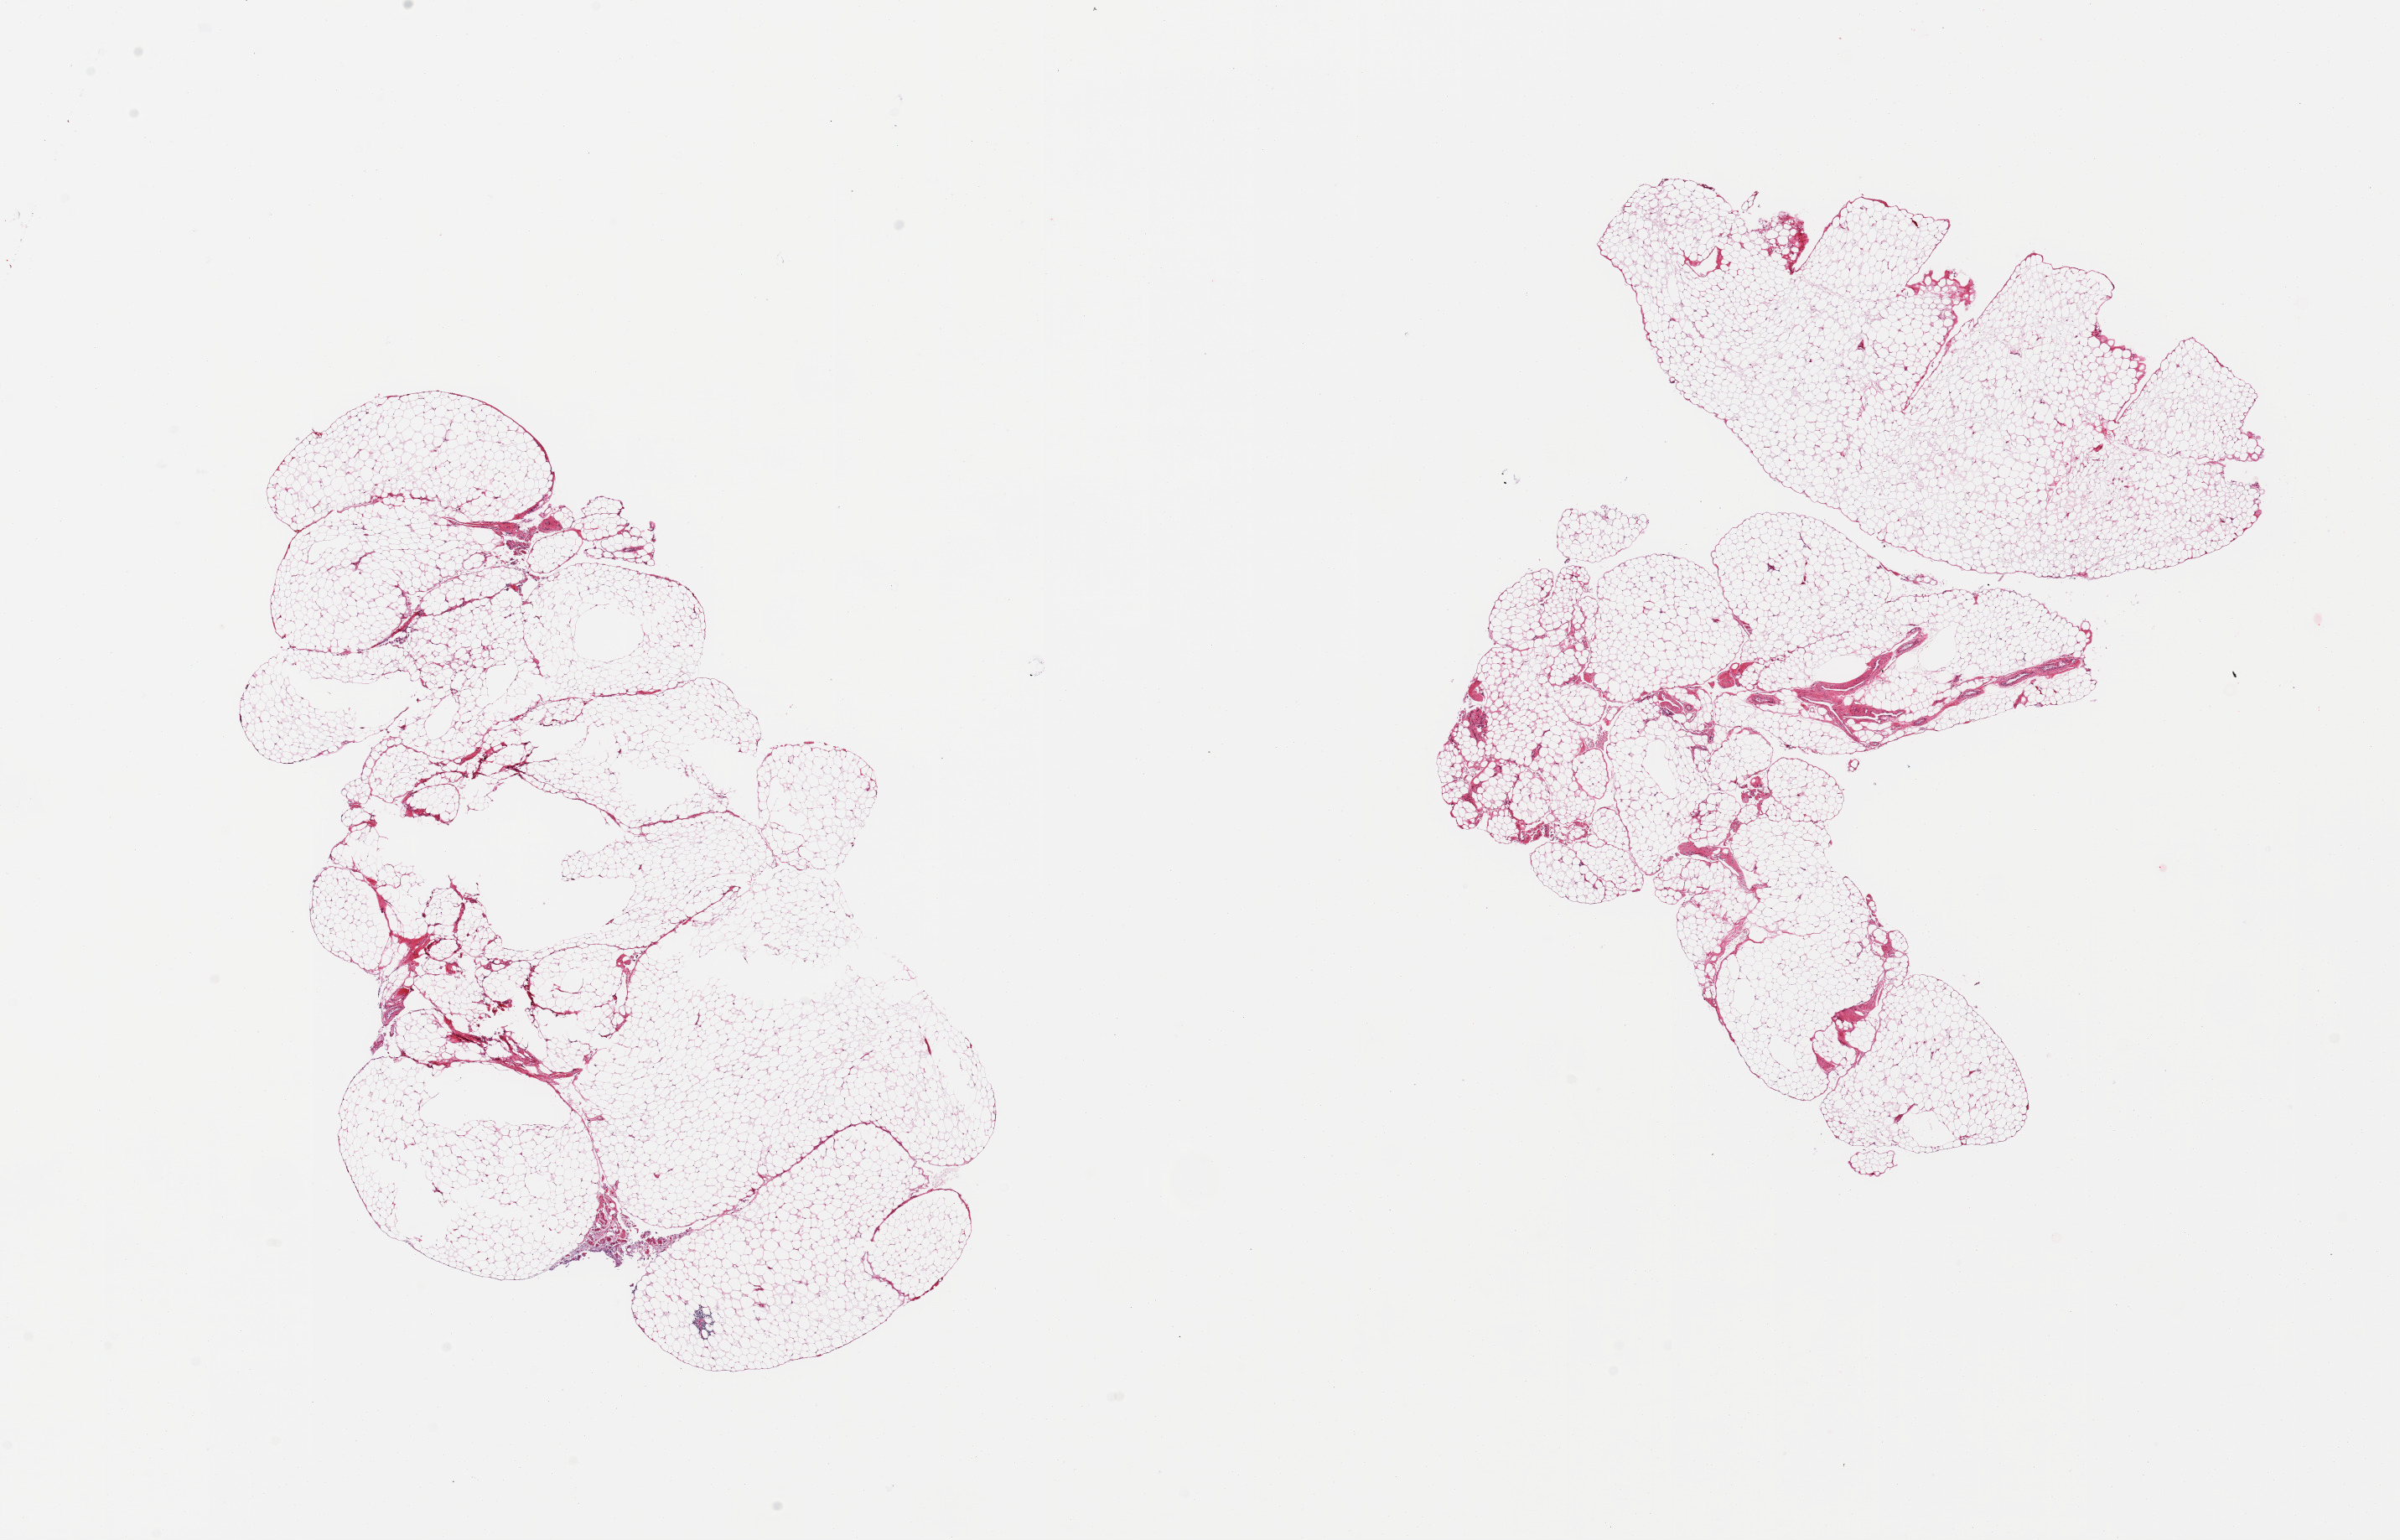
Whole-slide image, hematoxylin and eosin (H&E) stain — whole scanned area (about 22.6 x 14.5 mm, from a 20x scan) shown as a low-resolution overview; PAXgene-fixed paraffin-embedded (PFPE) section; target tissue: omentum; donor tissue sample. Donor: male.
Review note (as recorded): 2 pieces, ~5-10% interstitial fascia/mesothelium/vascular elements.